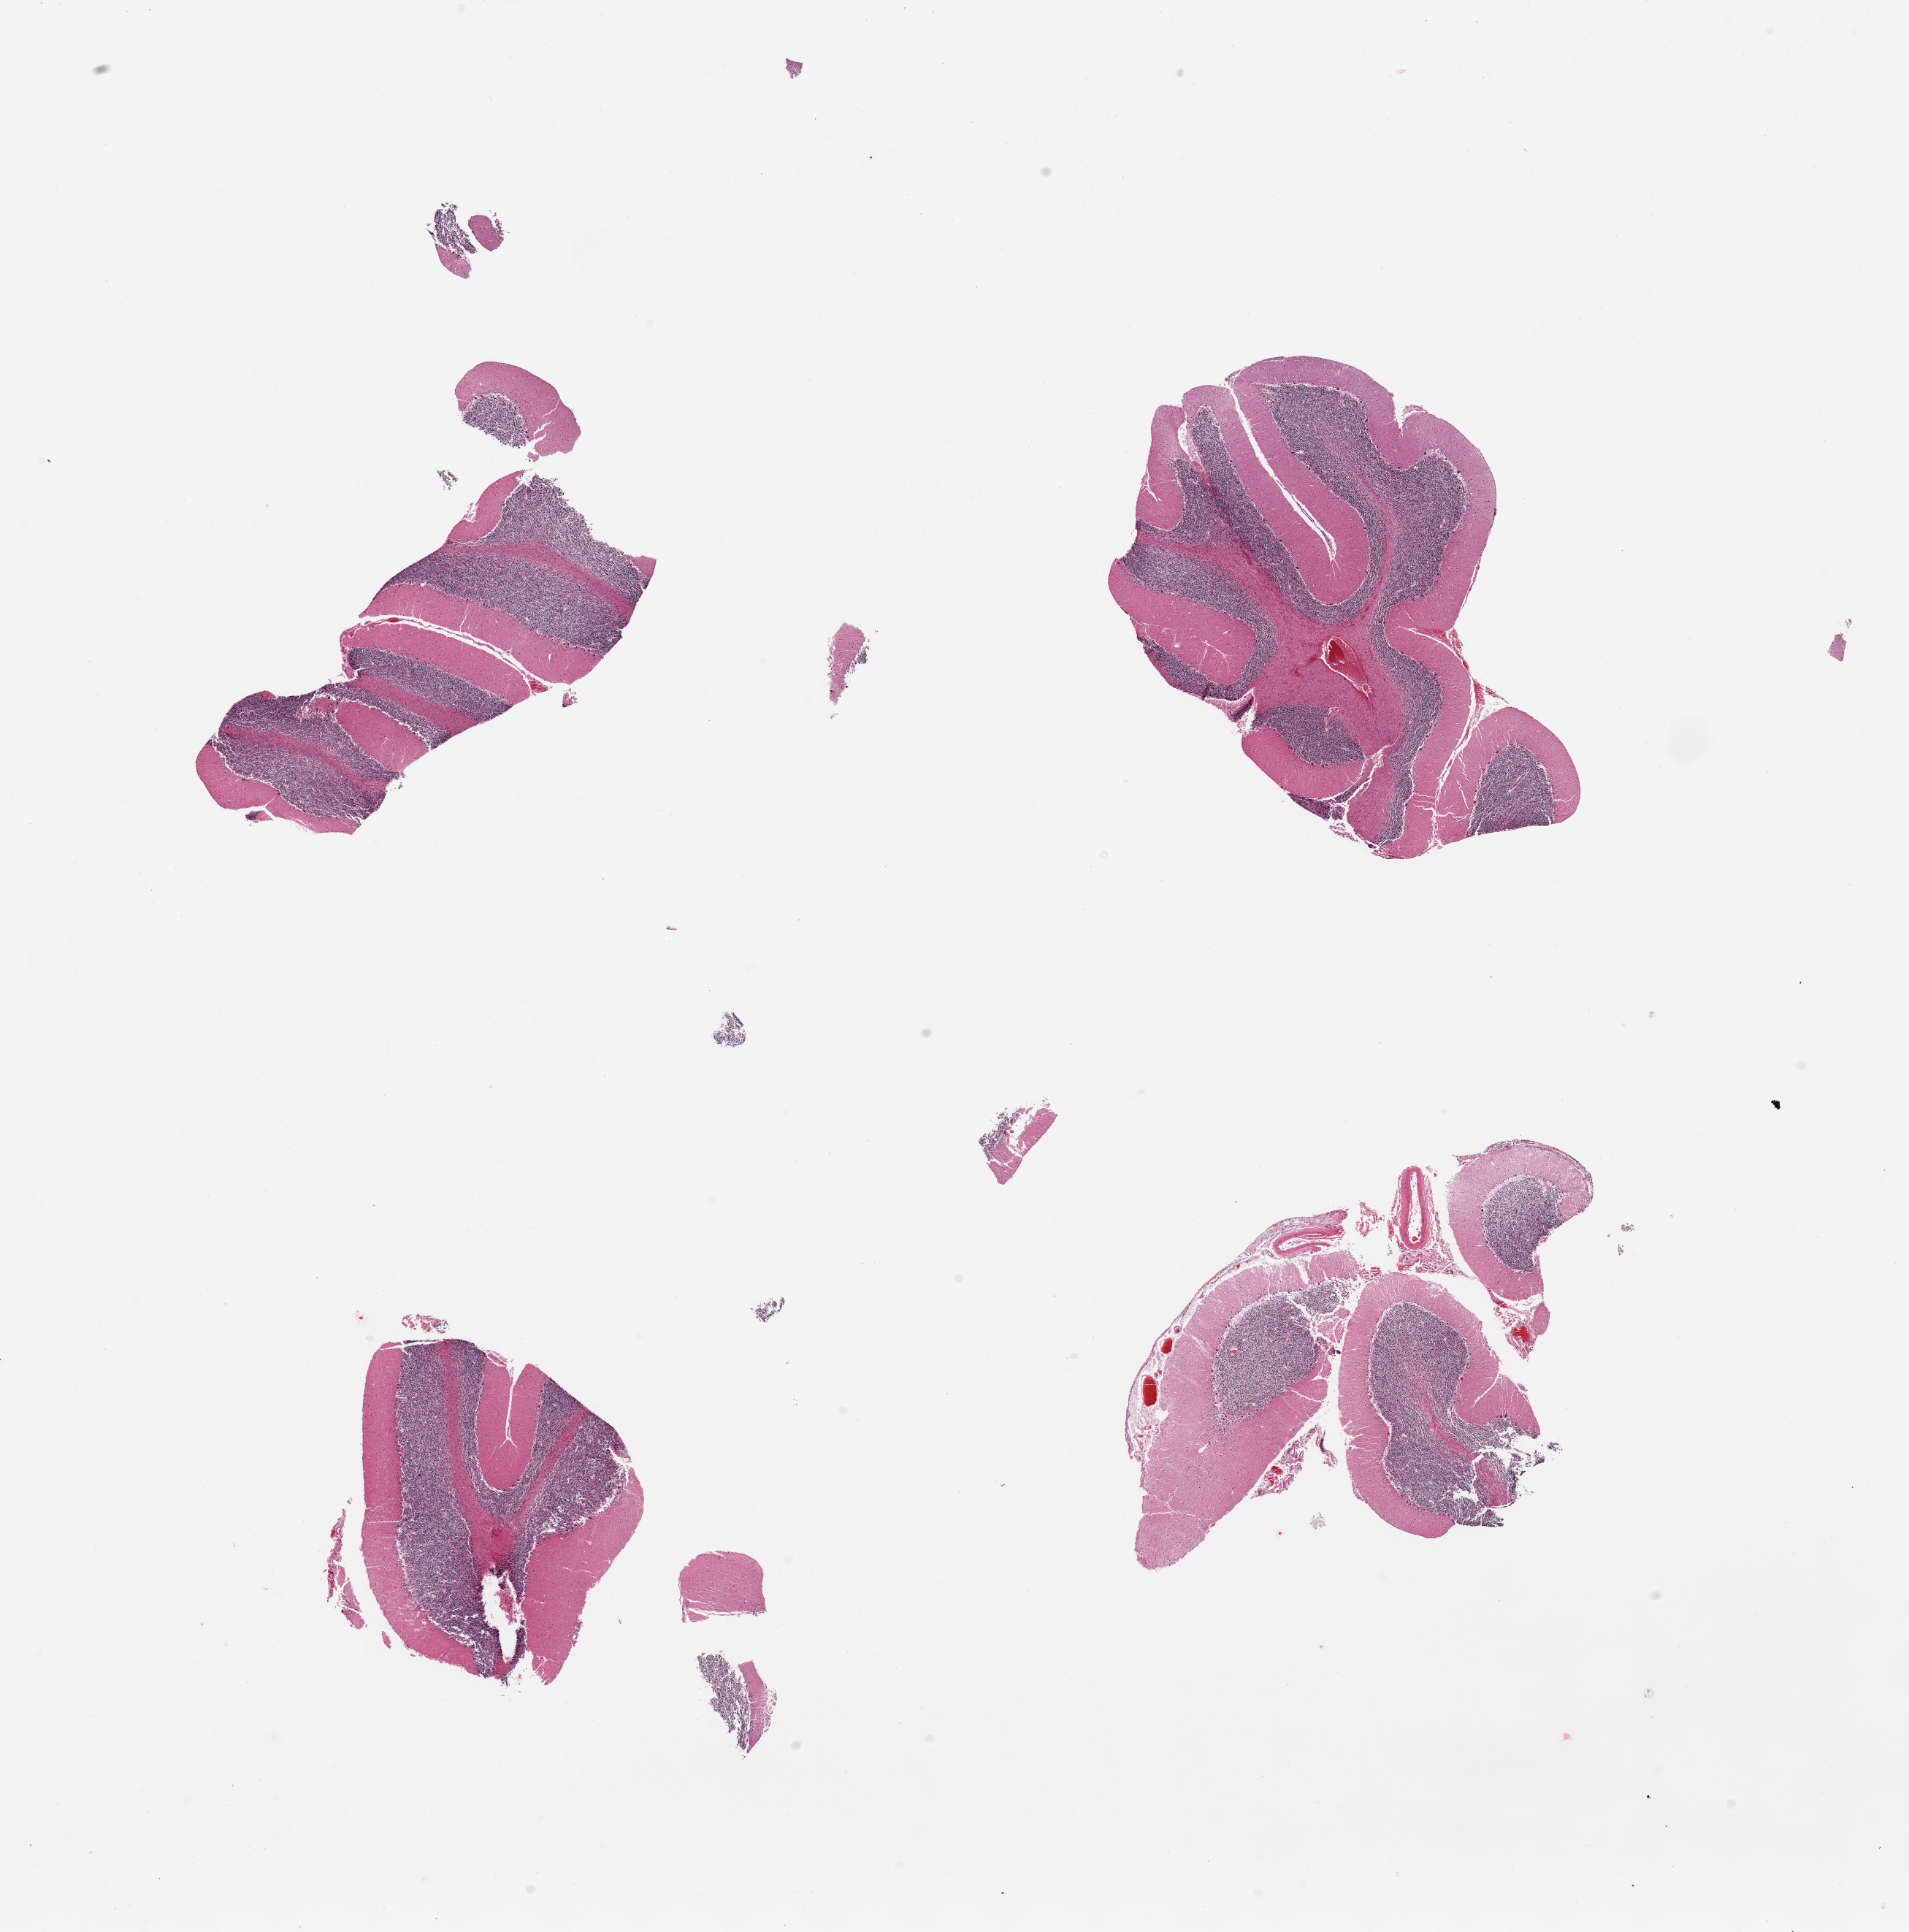
Whole-slide image, hematoxylin and eosin (H&E) stain — whole scanned area (about 20.7 x 20.9 mm) shown as a low-resolution overview, PAXgene-fixed paraffin-embedded (PFPE) section, sampled site (target tissue): cerebellum, tissue donor sample. Donor: female.
Reviewer comment on this tissue sample: 4 pieces; Purkinje cells with some evidence of hypoxic change.